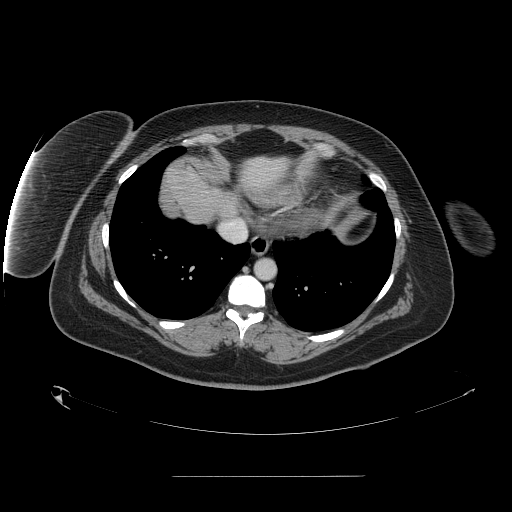
Contrast-enhanced abdominal CT, one axial slice. Position 143 of 164 along the scan axis. 120 kVp. Soft-tissue window (W 400 / L 40 HU). 512 × 512 image matrix, field of view 495 × 495 mm. Female patient, age 52 years. Case-level facts recorded for this patient, not image findings: diagnosis: colorectal cancer liver metastases, imaged before liver resection; multiple liver metastases: yes; largest metastasis: 3.5 cm; disease in both lobes: no.
Outlined on this slice (expert manual segmentation):
- liver: box from (x=170, y=168) to (x=236, y=224) px
- planned liver remnant (the part of the liver to remain after resection): (x=192, y=174)–(x=237, y=215)